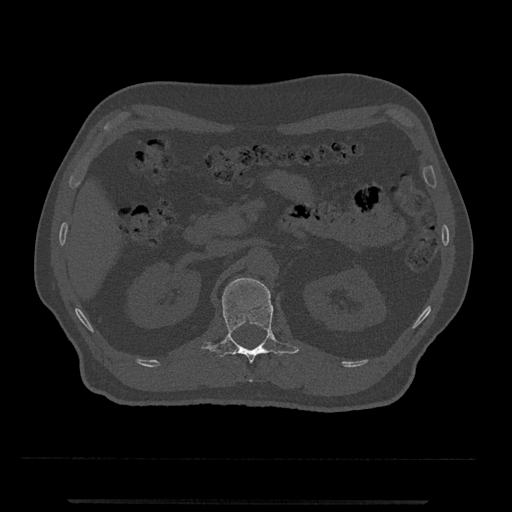
CT including the spine, one axial slice. Bone window (W 1800 / L 400 HU). 0.5 mm slice thickness. 512 × 512 image matrix, field of view 419 × 419 mm. Patient: male, 63 years. Case-level facts recorded for this patient, not image findings: primary cancer: prostate.
Outlined on this slice (semi-automatically segmented with operator editing):
- L1 vertebra: bounding box (x1, y1, x2, y2) in pixels: (201, 278, 299, 382)